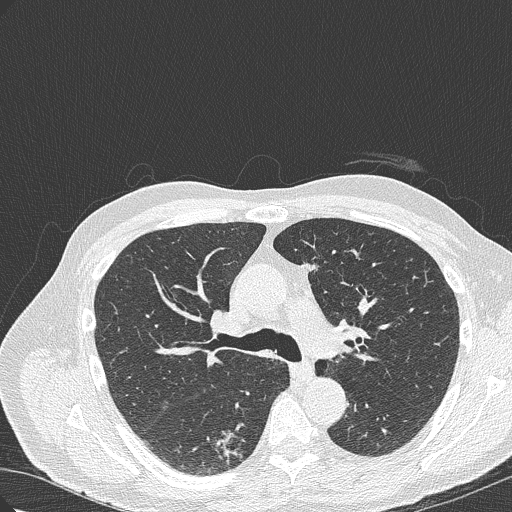
Axial slice from a low-dose chest CT screening exam. First (baseline) screen. Lung window (W 1500 / L -600 HU). 1 mm slice thickness. Slice 113 of 322 in the series. 512 × 512 image matrix, field of view 350 × 350 mm. Male participant, aged 70 years at enrolment.
Lesion marked by an expert reader, bounding box <201,419,265,467> (left, top, right, bottom; pixels). The screening reader recorded 4 non-calcified nodules or masses ≥4 mm on this exam; which of them this box marks is not recorded.